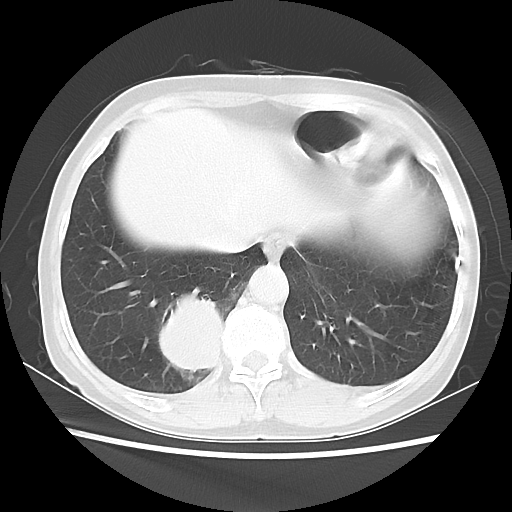
Chest CT, one axial slice. Slice 12 of 56 in the series (ordered by position). Reconstruction kernel LUNG. Lung window (W 1500 / L -600 HU). 5 mm slice thickness. 512 × 512 image matrix, field of view 332 × 332 mm. Patient: female, 66 years. Case-level facts recorded for this patient, not image findings: clinical TNM (as recorded): T2 N3 M0; histopathological grade: G3.
Outlined on this slice (bounding box drawn by a radiologist):
- lung tumour (recorded histology: small cell carcinoma): bounding box <154,297,231,372> (left, top, right, bottom; pixels)